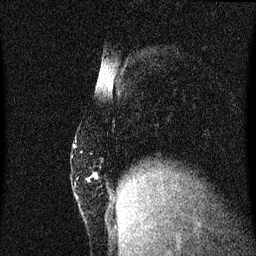
Breast MRI (dynamic contrast-enhanced), one sagittal slice; slice 13 of 60 in the series (ordered by position); dynamic contrast-enhanced series, image 2 of 3 at this slice position (ordered by acquisition); 1.5 T; TE 4.2 ms, TR 8.4 ms; 2 mm slice thickness; 256 × 256 image matrix. Female patient, age 52 years. Case-level facts recorded for this patient, not image findings: setting: breast cancer imaged before/during neoadjuvant chemotherapy; receptor status: HER2-positive.
Outlined on this slice (semi-automatically segmented with operator editing):
- analysis volume of interest (the breast-tissue region the enhancement analysis was run in; not a lesion): bounding box (x1, y1, x2, y2) in pixels: (72, 124, 117, 191)
- tumour enhancement mask (voxels above the 70 % enhancement threshold inside the analysis volume of interest): (93, 174, 96, 177)